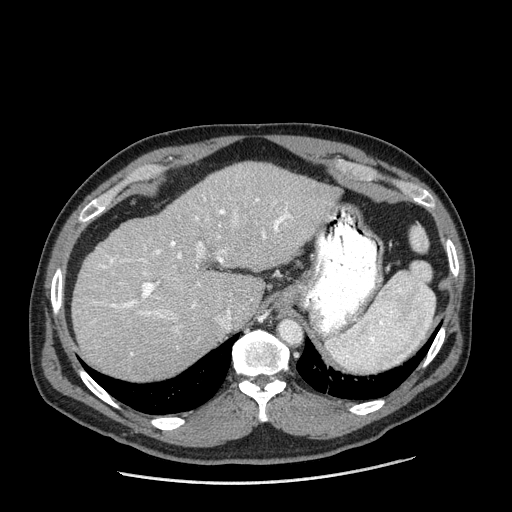
Contrast-enhanced abdominal CT (liver protocol), one axial slice. Slice 137 of 198 in the series (ordered by position). Reconstruction kernel STANDARD. 120 kVp. One of 2 acquisitions stored at this slice position. Soft-tissue window (W 400 / L 40 HU). 2.5 mm slice thickness. 512 × 512 image matrix. From the clinical record (not read from this slice): diagnosis: hepatocellular carcinoma (patient treated with transarterial chemoembolisation; whether this scan precedes or follows treatment is not stated here); TNM stage (as recorded): Stage-II; Child-Pugh class: A; tumour differentiation: moderately differentiated.
Outlined on this slice (semi-automatic segmentation, software-assisted and operator-edited):
- liver parenchyma outside the tumour (the mass and vessels are separate outlines, so this box may not span the whole liver): bounding box [x1, y1, x2, y2] px = [72, 162, 337, 380]
- liver vessels: [93, 196, 293, 356]